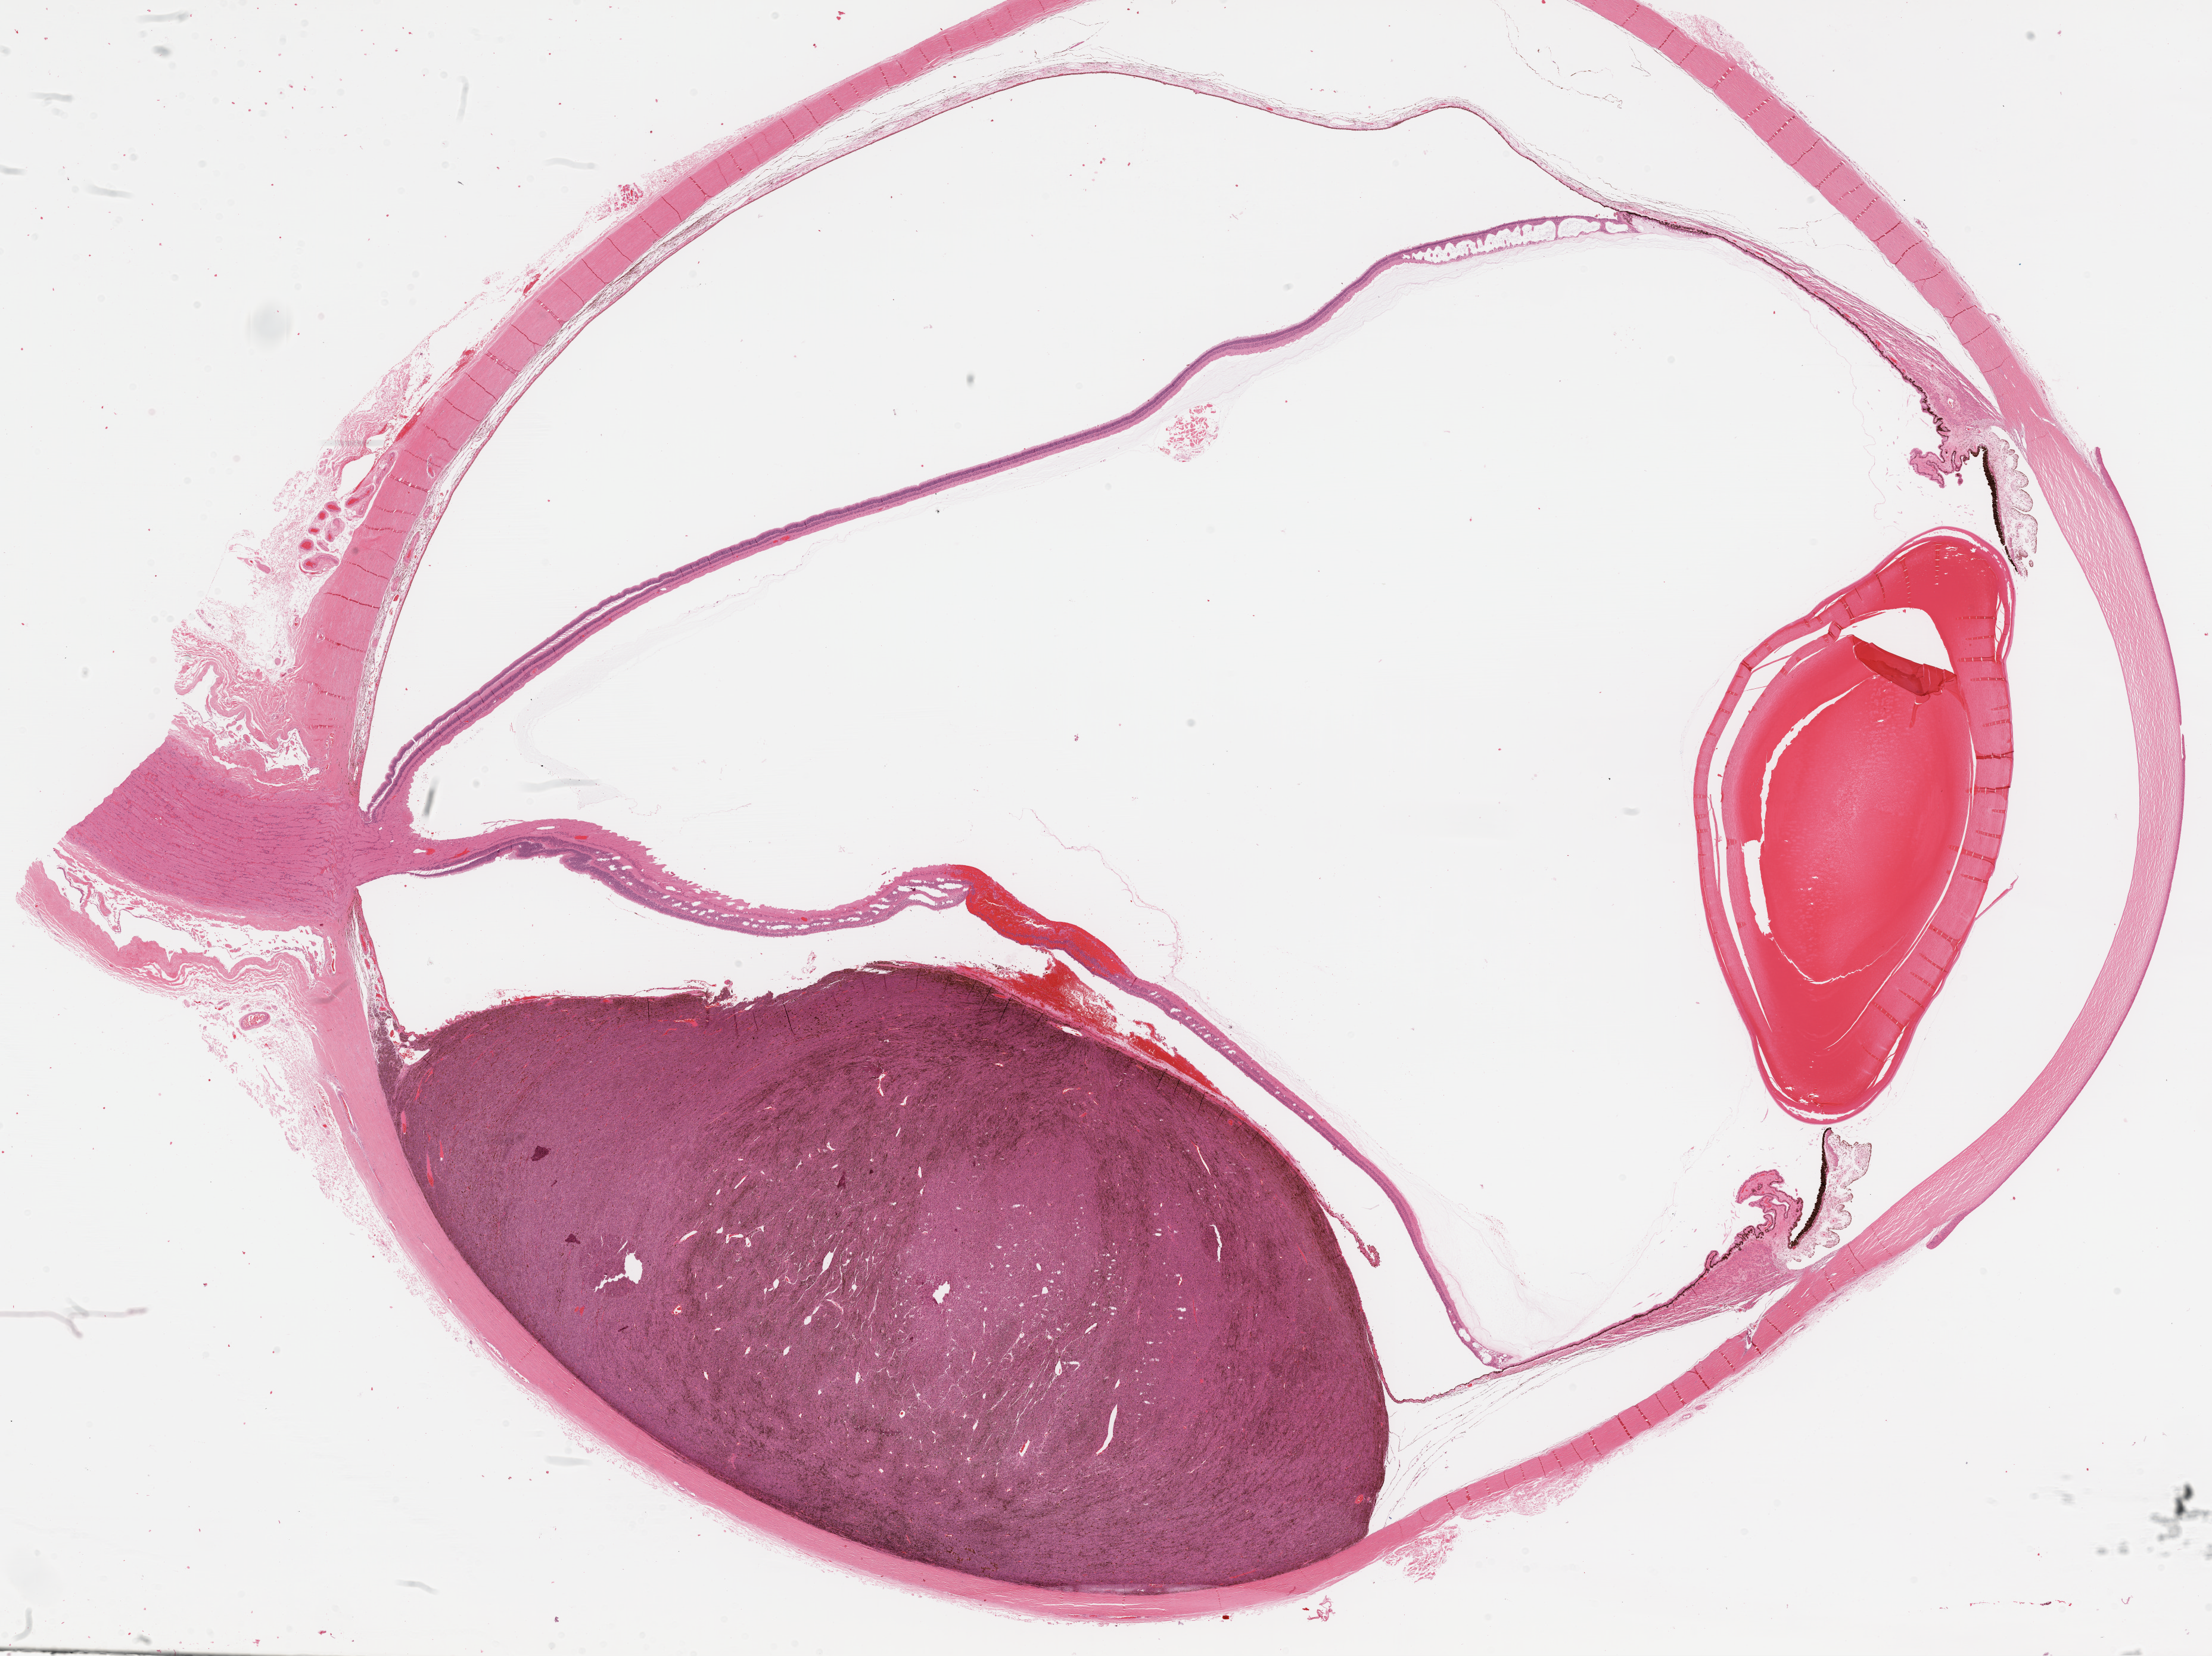
Digitized H&E tissue section (whole slide) — shown as a low-resolution overview of the whole scanned area (about 29.9 x 22.4 mm, acquisition: 20x scan). FFPE section. Primary tumour sample from the uvea. Male, age 54 years at initial diagnosis.
AJCC pathologic stage: IIIA. Histologic diagnosis: Spindle cell melanoma, type B (choroid).